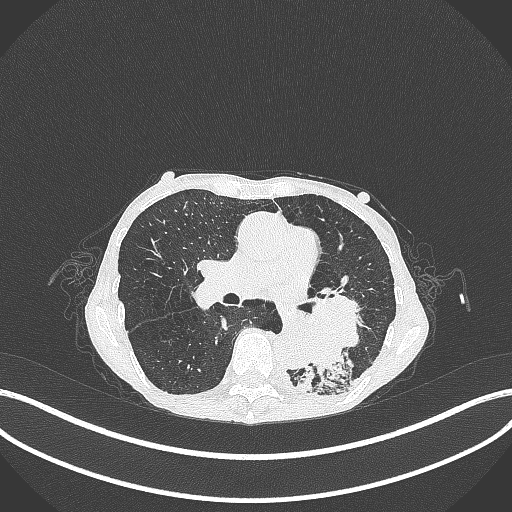
Chest CT, one axial slice; position 146 of 347 along the scan axis; reconstruction kernel B70f; lung window (W 1500 / L -600 HU); 1 mm slice thickness; 512 × 512 image matrix. Female patient, age 70 years. From the clinical record (not read from this slice): clinical TNM (as recorded): T3 N0 M0; histopathological grade: G3.
Structures marked on this image (bounding box drawn by a radiologist):
- lung tumour (recorded histology: small cell carcinoma): bounding box (x1, y1, x2, y2) in pixels: (290, 289, 369, 377)